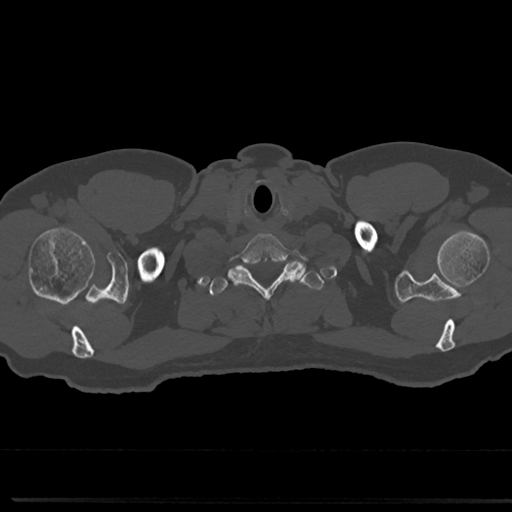
CT including the spine, one axial slice. Slice 694 of 817 in the series (ordered by position). Reconstruction kernel Br40s/3. 120 kVp. Bone window (W 1800 / L 400 HU). 0.5 mm slice thickness. 512 × 512 image matrix. Patient: male, 61 years. Case-level facts recorded for this patient, not image findings: primary cancer: prostate.
Outlined on this slice (semi-automatic segmentation, software-assisted and operator-edited):
- T1 vertebra: bounding box [x1, y1, x2, y2] px = [209, 262, 319, 342]